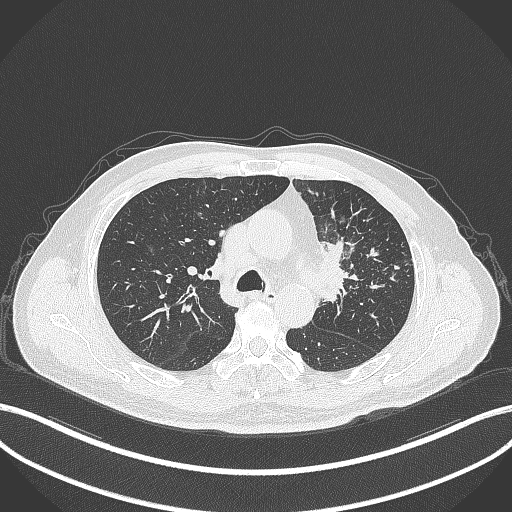
Chest CT, one axial slice; position 232 of 386 along the scan axis; 120 kVp; lung window (W 1500 / L -600 HU); 512 × 512 image matrix. Patient: male, 69 years. Case-level facts recorded for this patient, not image findings: clinical TNM (as recorded): T2a N2 M0.
Structures marked on this image (rectangle marked by the reading radiologist):
- lung tumour (recorded histology: adenocarcinoma): bounding box [x1, y1, x2, y2] px = [313, 228, 351, 286]